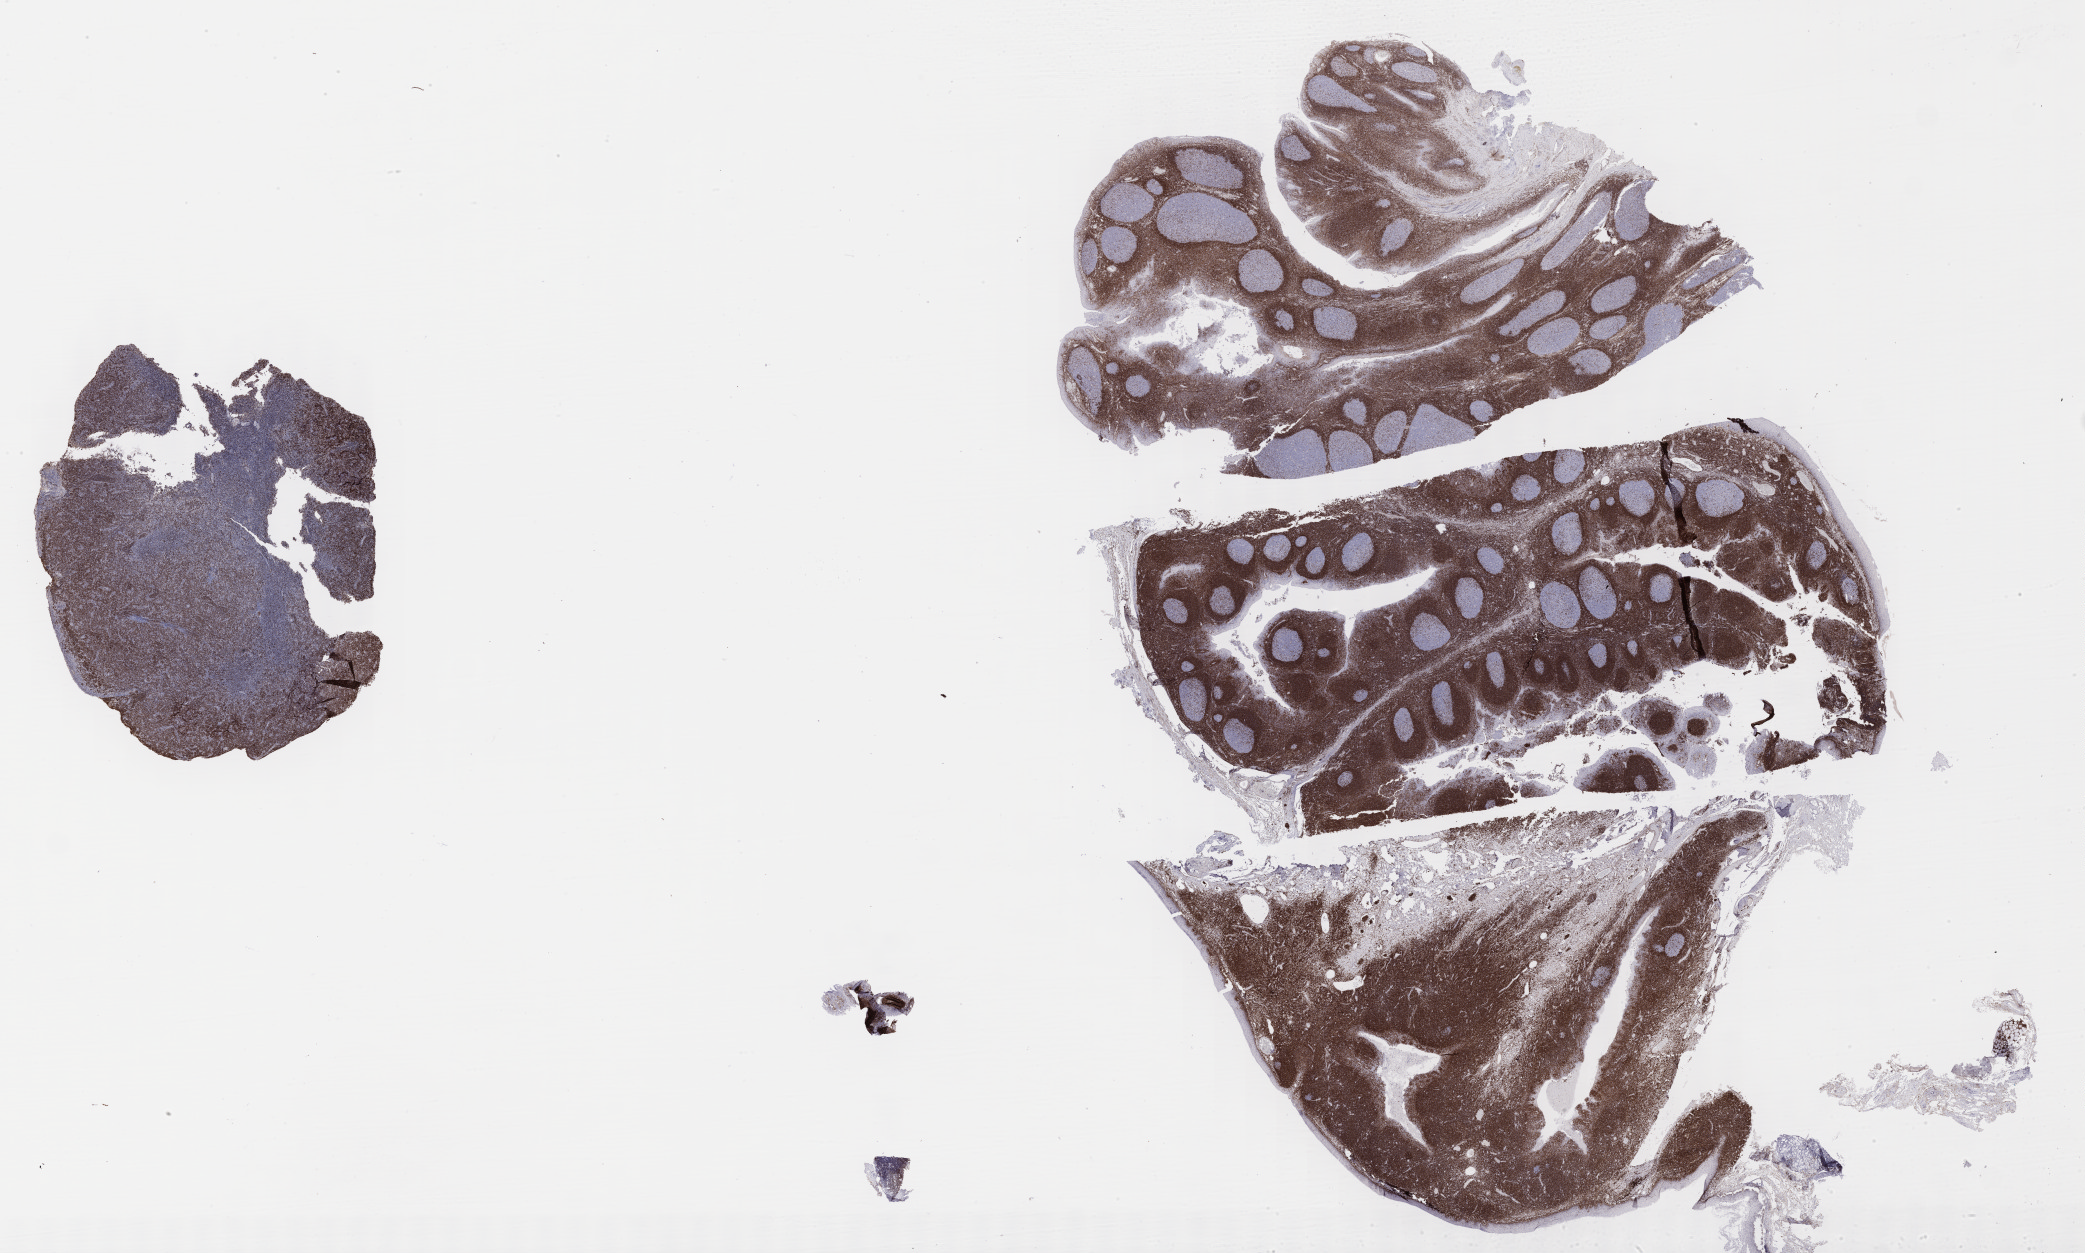
Immunohistochemistry (IHC) whole-slide image stained for BCL2, low-resolution overview of the scanned area, about 33.7 x 20.3 mm. Specimen: tumor tissue. Site: liver. Patient male; age 46 years.
Histologic diagnosis: Diffuse large B-cell lymphoma, NOS.